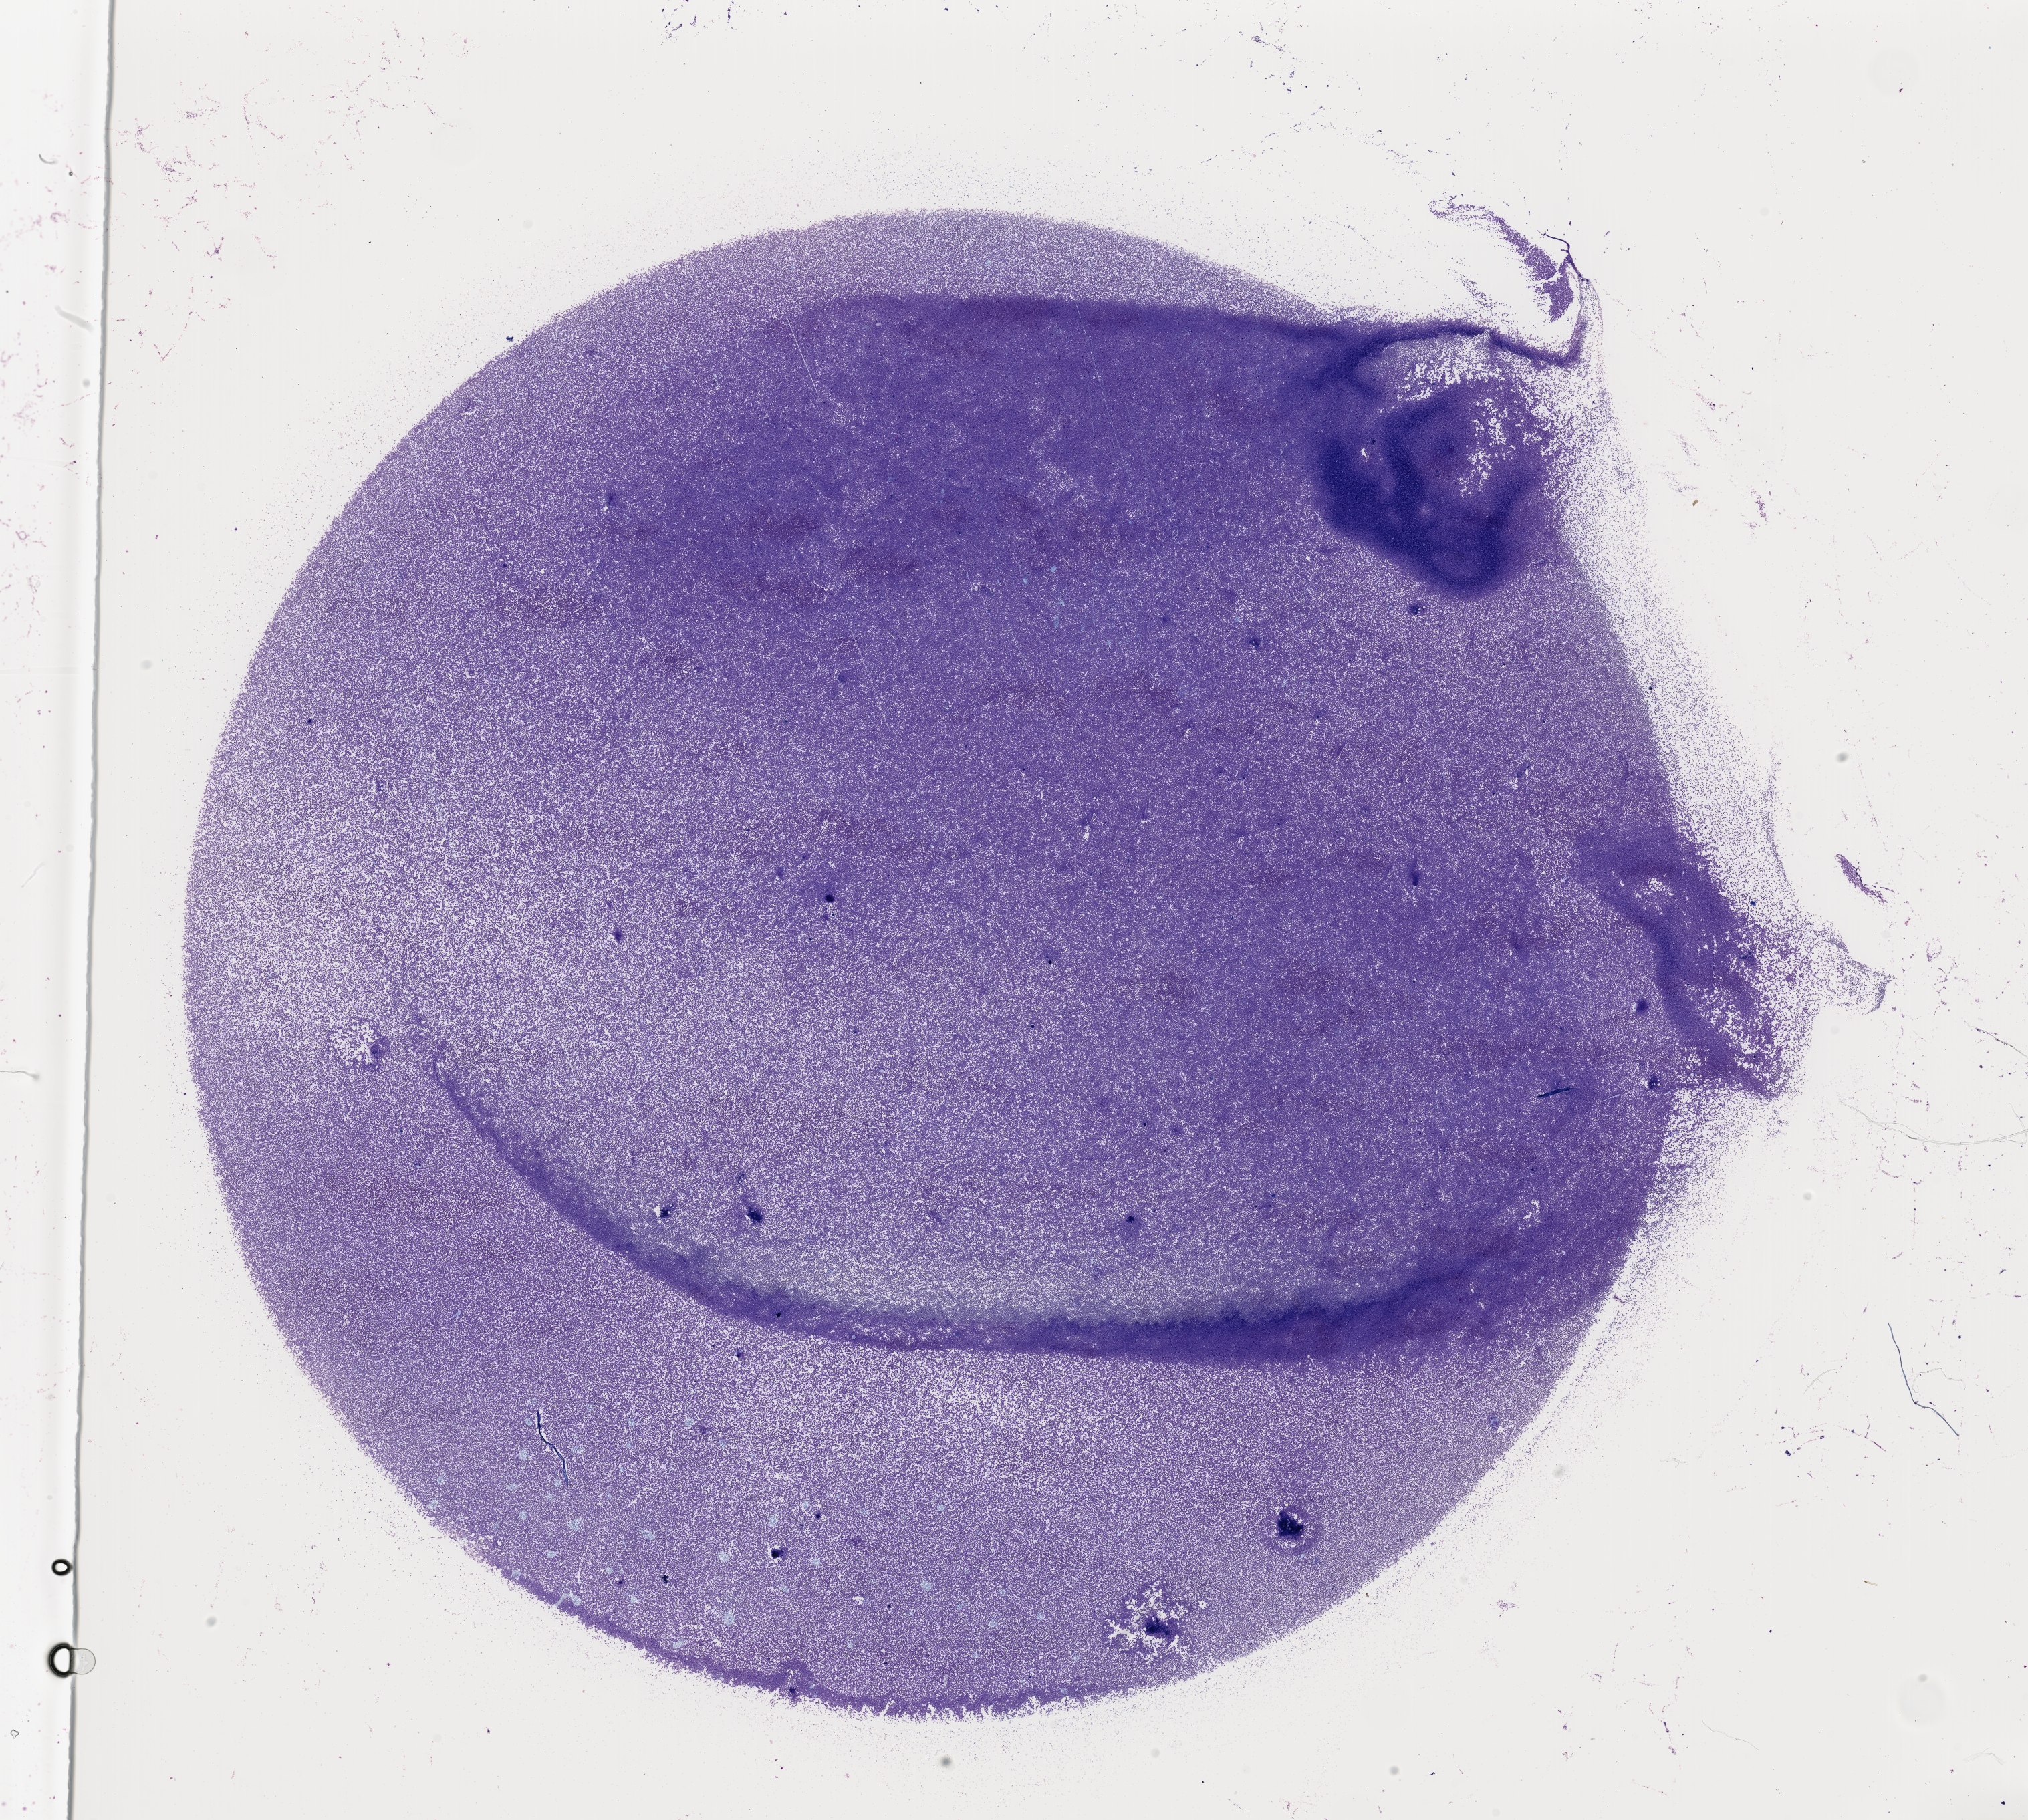
Digitized H&E-stained tissue section (whole slide), whole scanned area (about 24.0 x 21.5 mm, from a 40x scan) shown as a low-resolution overview; bone marrow (leukaemic) sample. Patient: female, age 61 years. Blasts: 99%.
Diagnosis: Acute Myeloid Leukemia. FAB classification: M0.